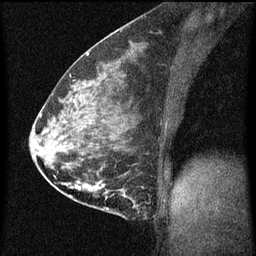
Breast MRI (dynamic contrast-enhanced), one sagittal slice; slice 29 of 60 in the series (ordered by position); dynamic contrast-enhanced series, image 2 of 3 at this slice position (ordered by acquisition); 1.5 T; TE 4.2 ms, TR 8 ms; 2 mm slice thickness; 256 × 256 image matrix, field of view 180 × 180 mm. Patient: female, 35 years.
Annotated regions visible in this slice (semi-automatic segmentation, software-assisted and operator-edited):
- analysis volume of interest (the breast-tissue region the enhancement analysis was run in; not a lesion): bounding box <110,186,141,219> (left, top, right, bottom; pixels)
- tumour enhancement mask (voxels above the 70 % enhancement threshold inside the analysis volume of interest): <121,190,136,207>